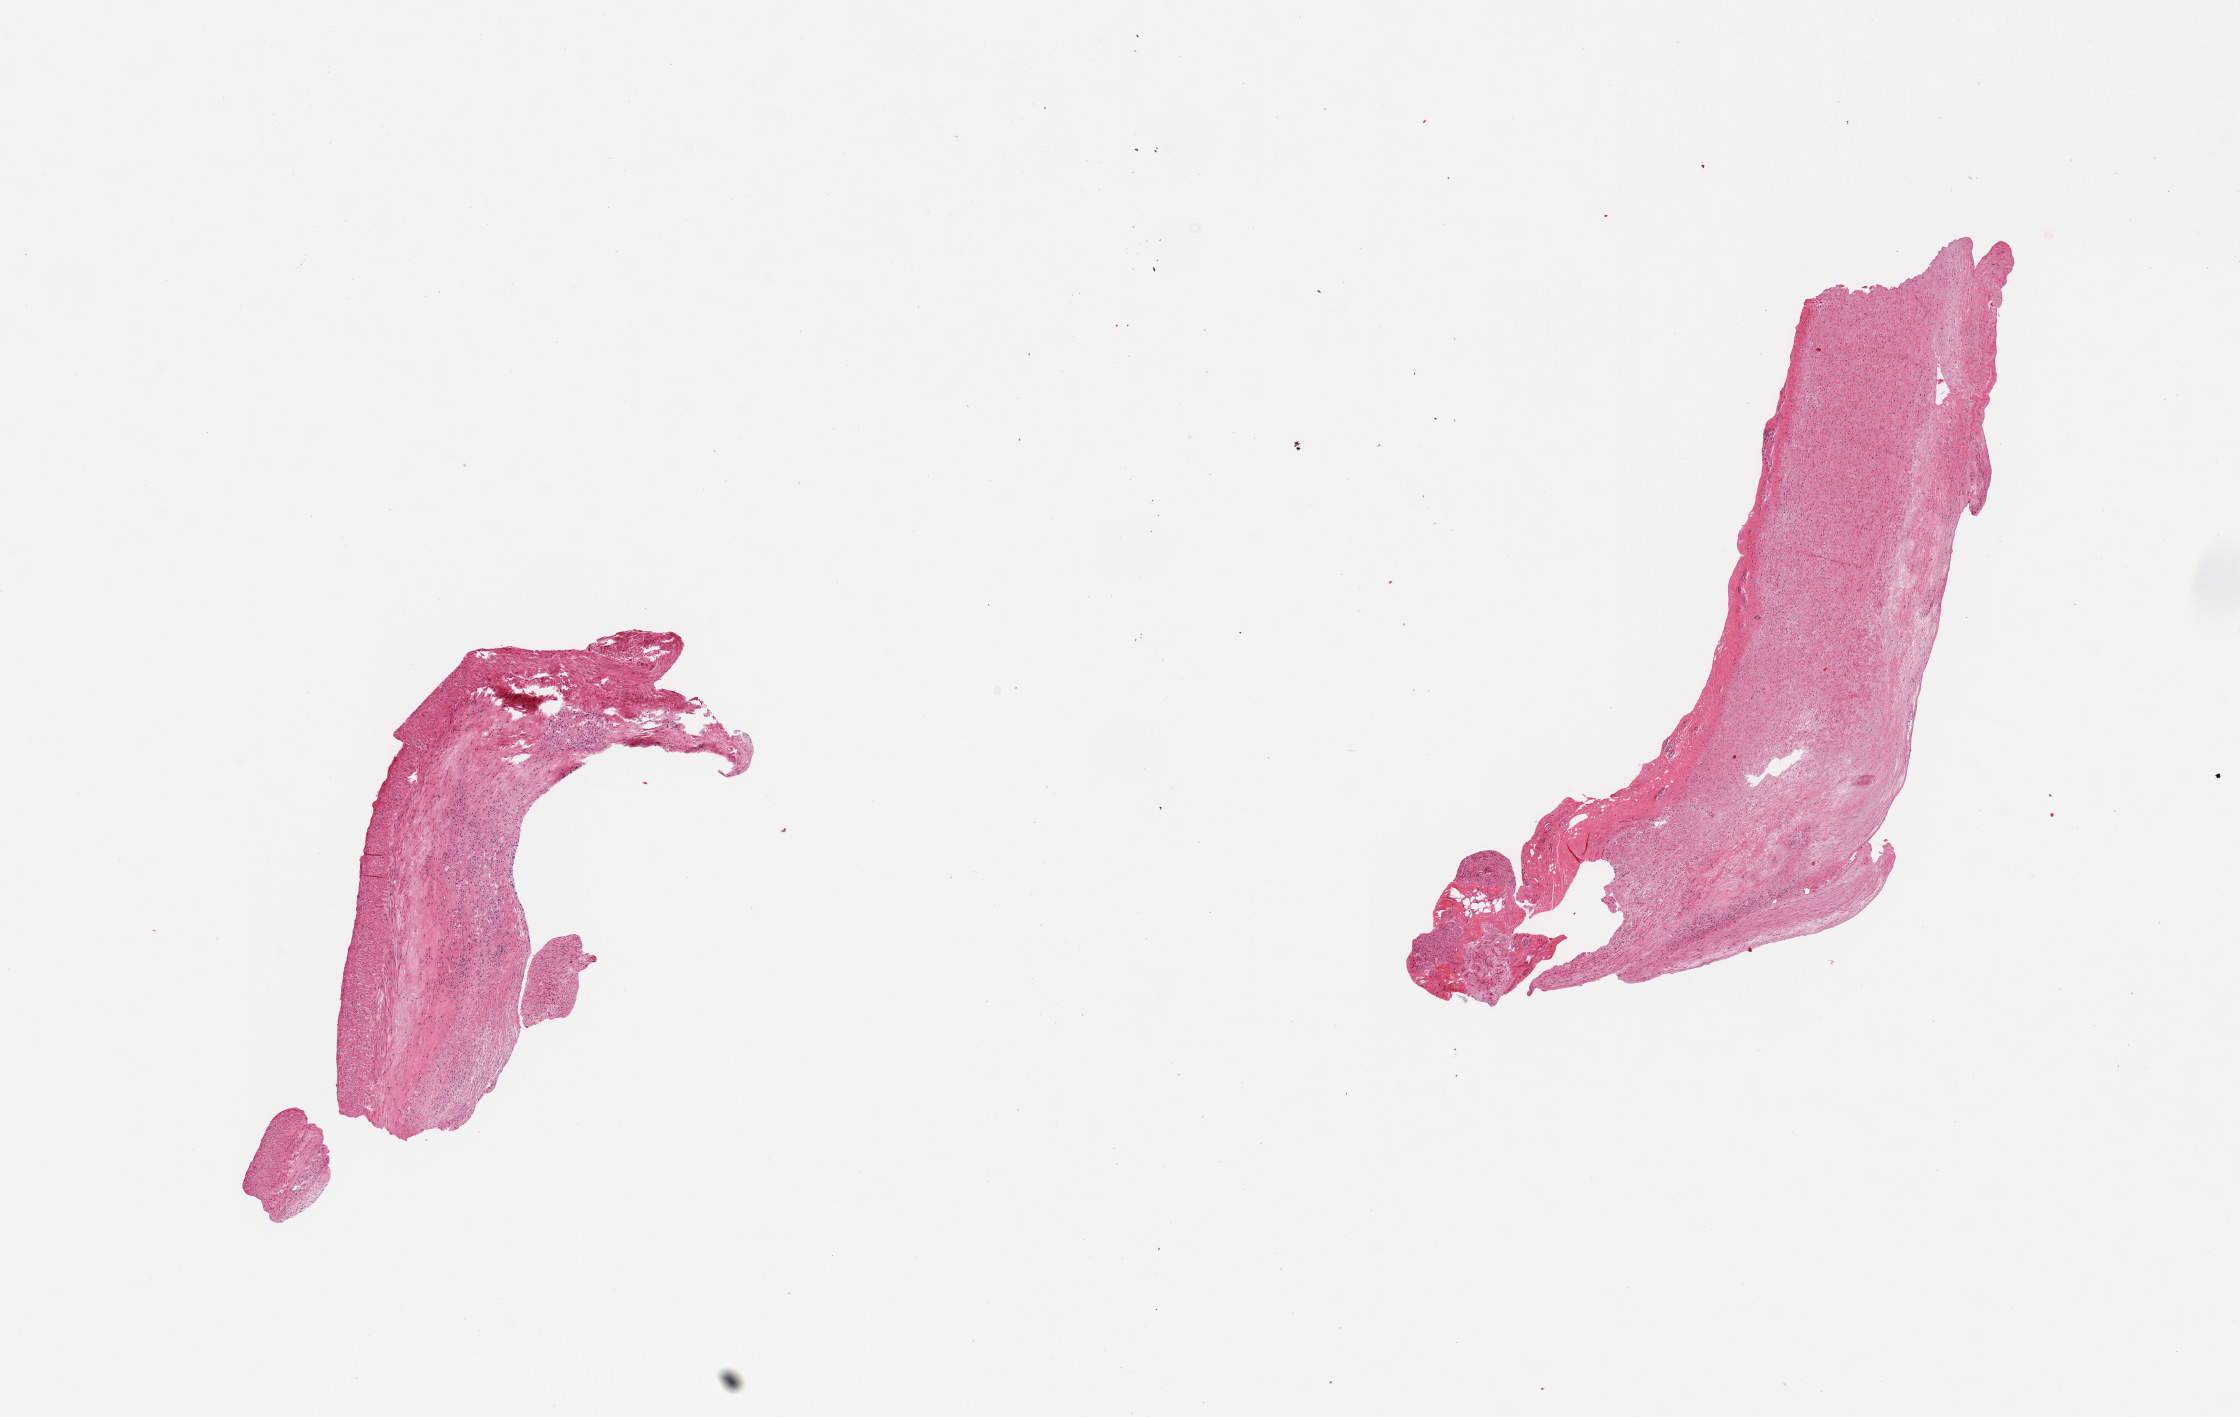
Digitized haematoxylin and eosin-stained section, low-resolution overview of the scanned area, about 17.7 x 11.2 mm. PAXgene-fixed paraffin-embedded (PFPE) section. Target tissue: coronary artery. Tissue donor sample.
Pathologist's review note for this sample: 2 pieces; fragment of arterial wall with atherosclerosis.